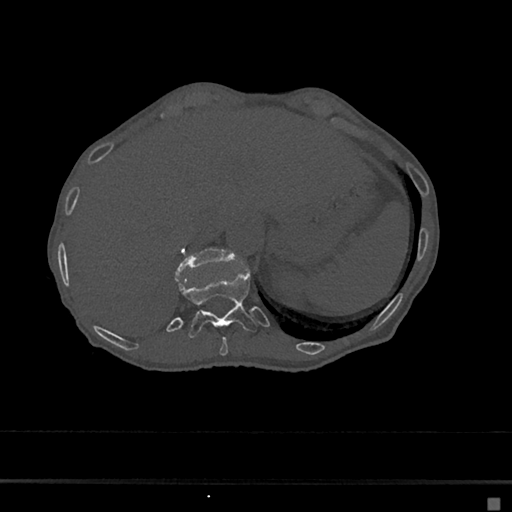
CT including the spine, one axial slice; position 174 of 797 along the scan axis; reconstruction kernel Br40s/3; 120 kVp; bone window (W 1800 / L 400 HU); 0.5 mm slice thickness; 512 × 512 image matrix. Female patient, age 68 years. From the clinical record (not read from this slice): primary cancer: renal.
Annotated regions visible in this slice (semi-automatically segmented with operator editing):
- T10 vertebra: bounding box <219,336,228,356> (left, top, right, bottom; pixels)
- T11 vertebra: <175,272,257,338>
- T12 vertebra: <175,247,234,277>